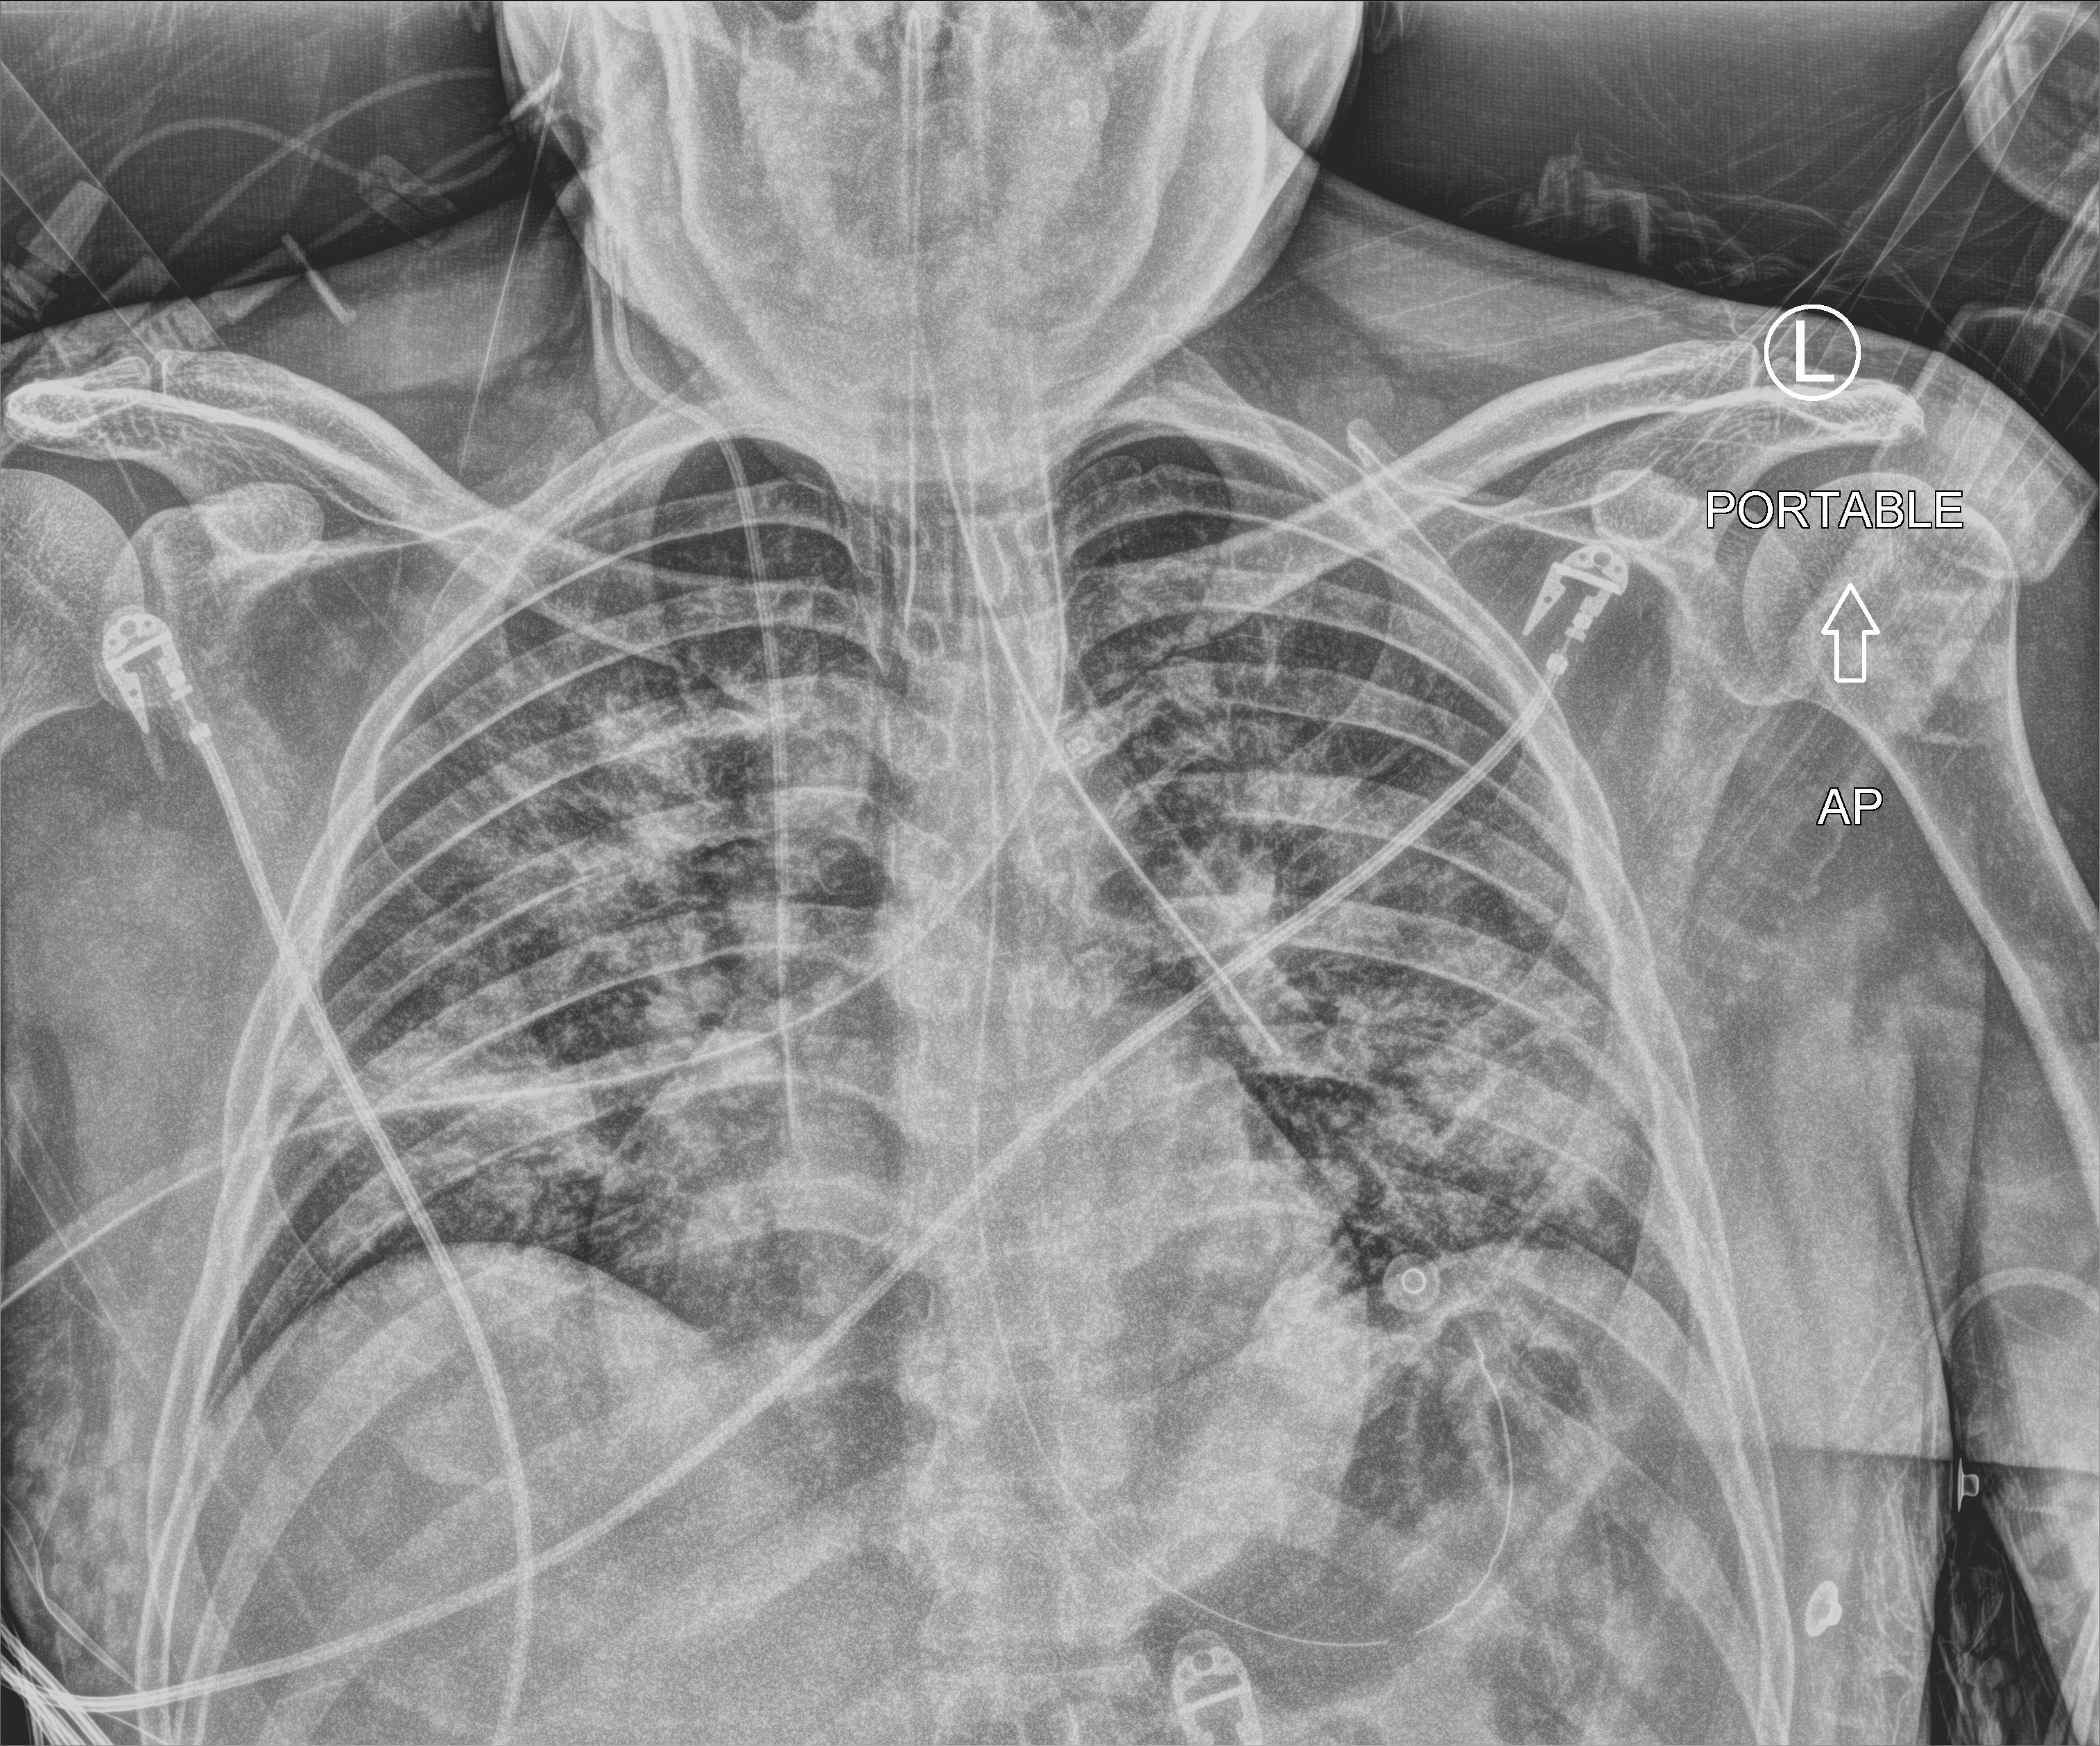
Portable chest radiograph; anteroposterior (AP) projection. Patient hospitalised with COVID-19; male, aged 18–59 years.
Admission-level facts for this patient (not findings on this image; timing relative to this image not recorded):
- length of hospital stay: 29 days
- mechanically ventilated during this hospital stay: yes